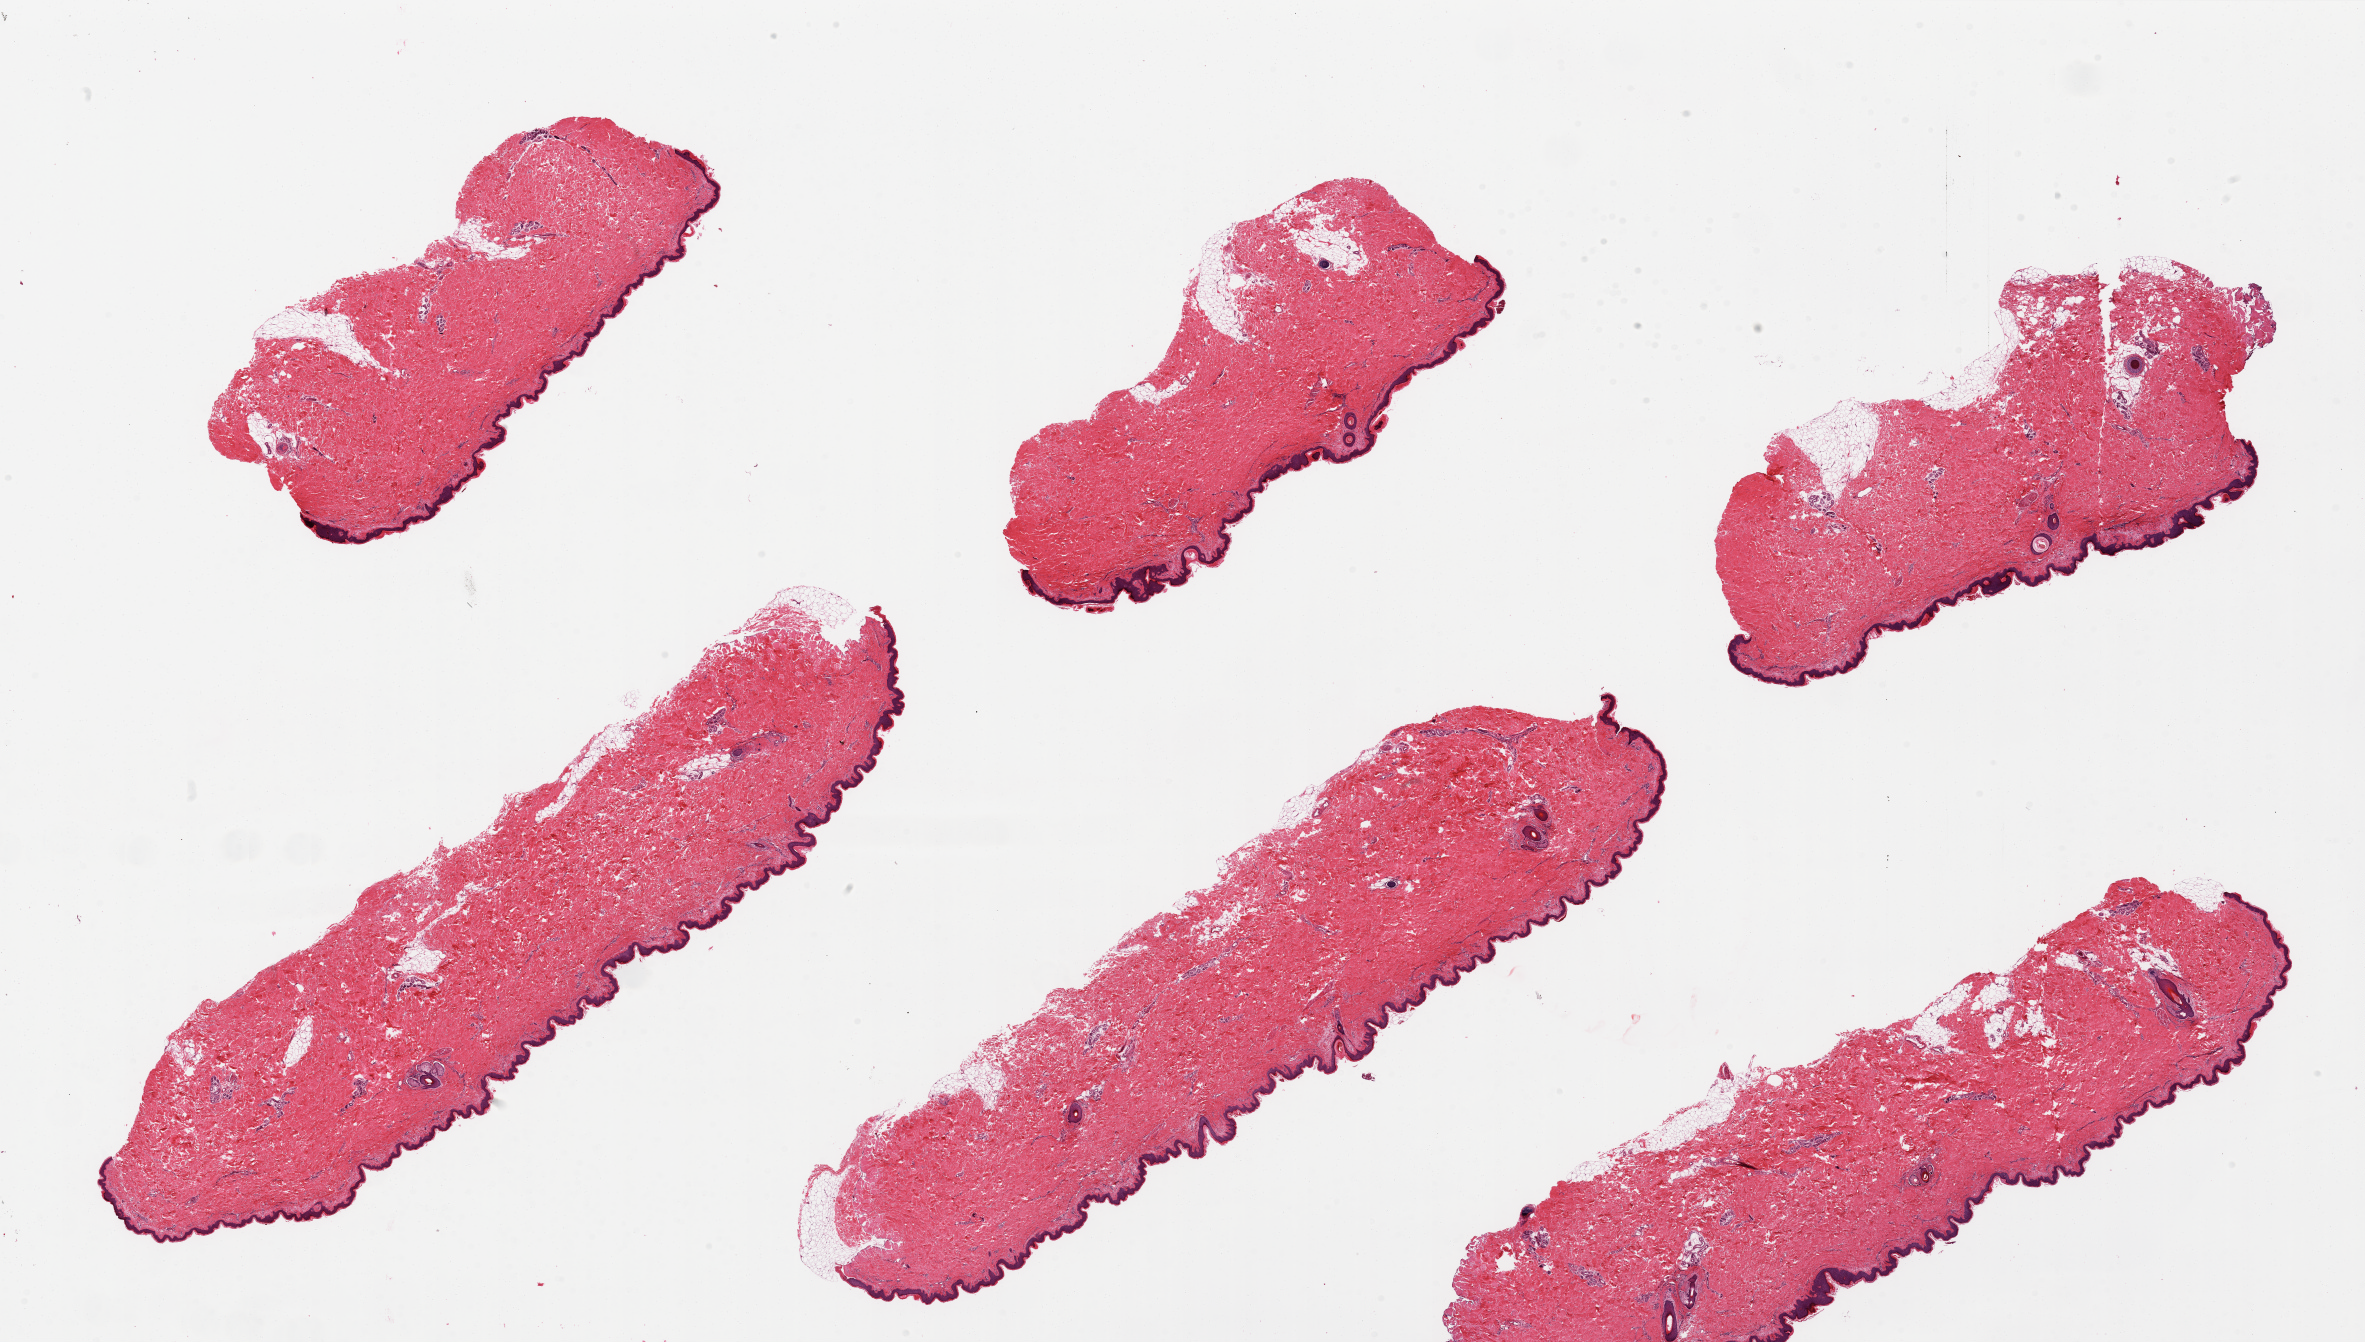
Digitized H&E-stained section, brightfield, a low-resolution overview of the entire scanned area, about 37.4 x 21.2 mm (slide scanned at 20x); PAXgene-fixed, paraffin-embedded tissue; sampled site (target tissue): skin of suprapubic region; donor tissue sample. Donor: male.
* reviewer comment on this tissue sample: 6 pieces, well trimmed with only scant attached fat